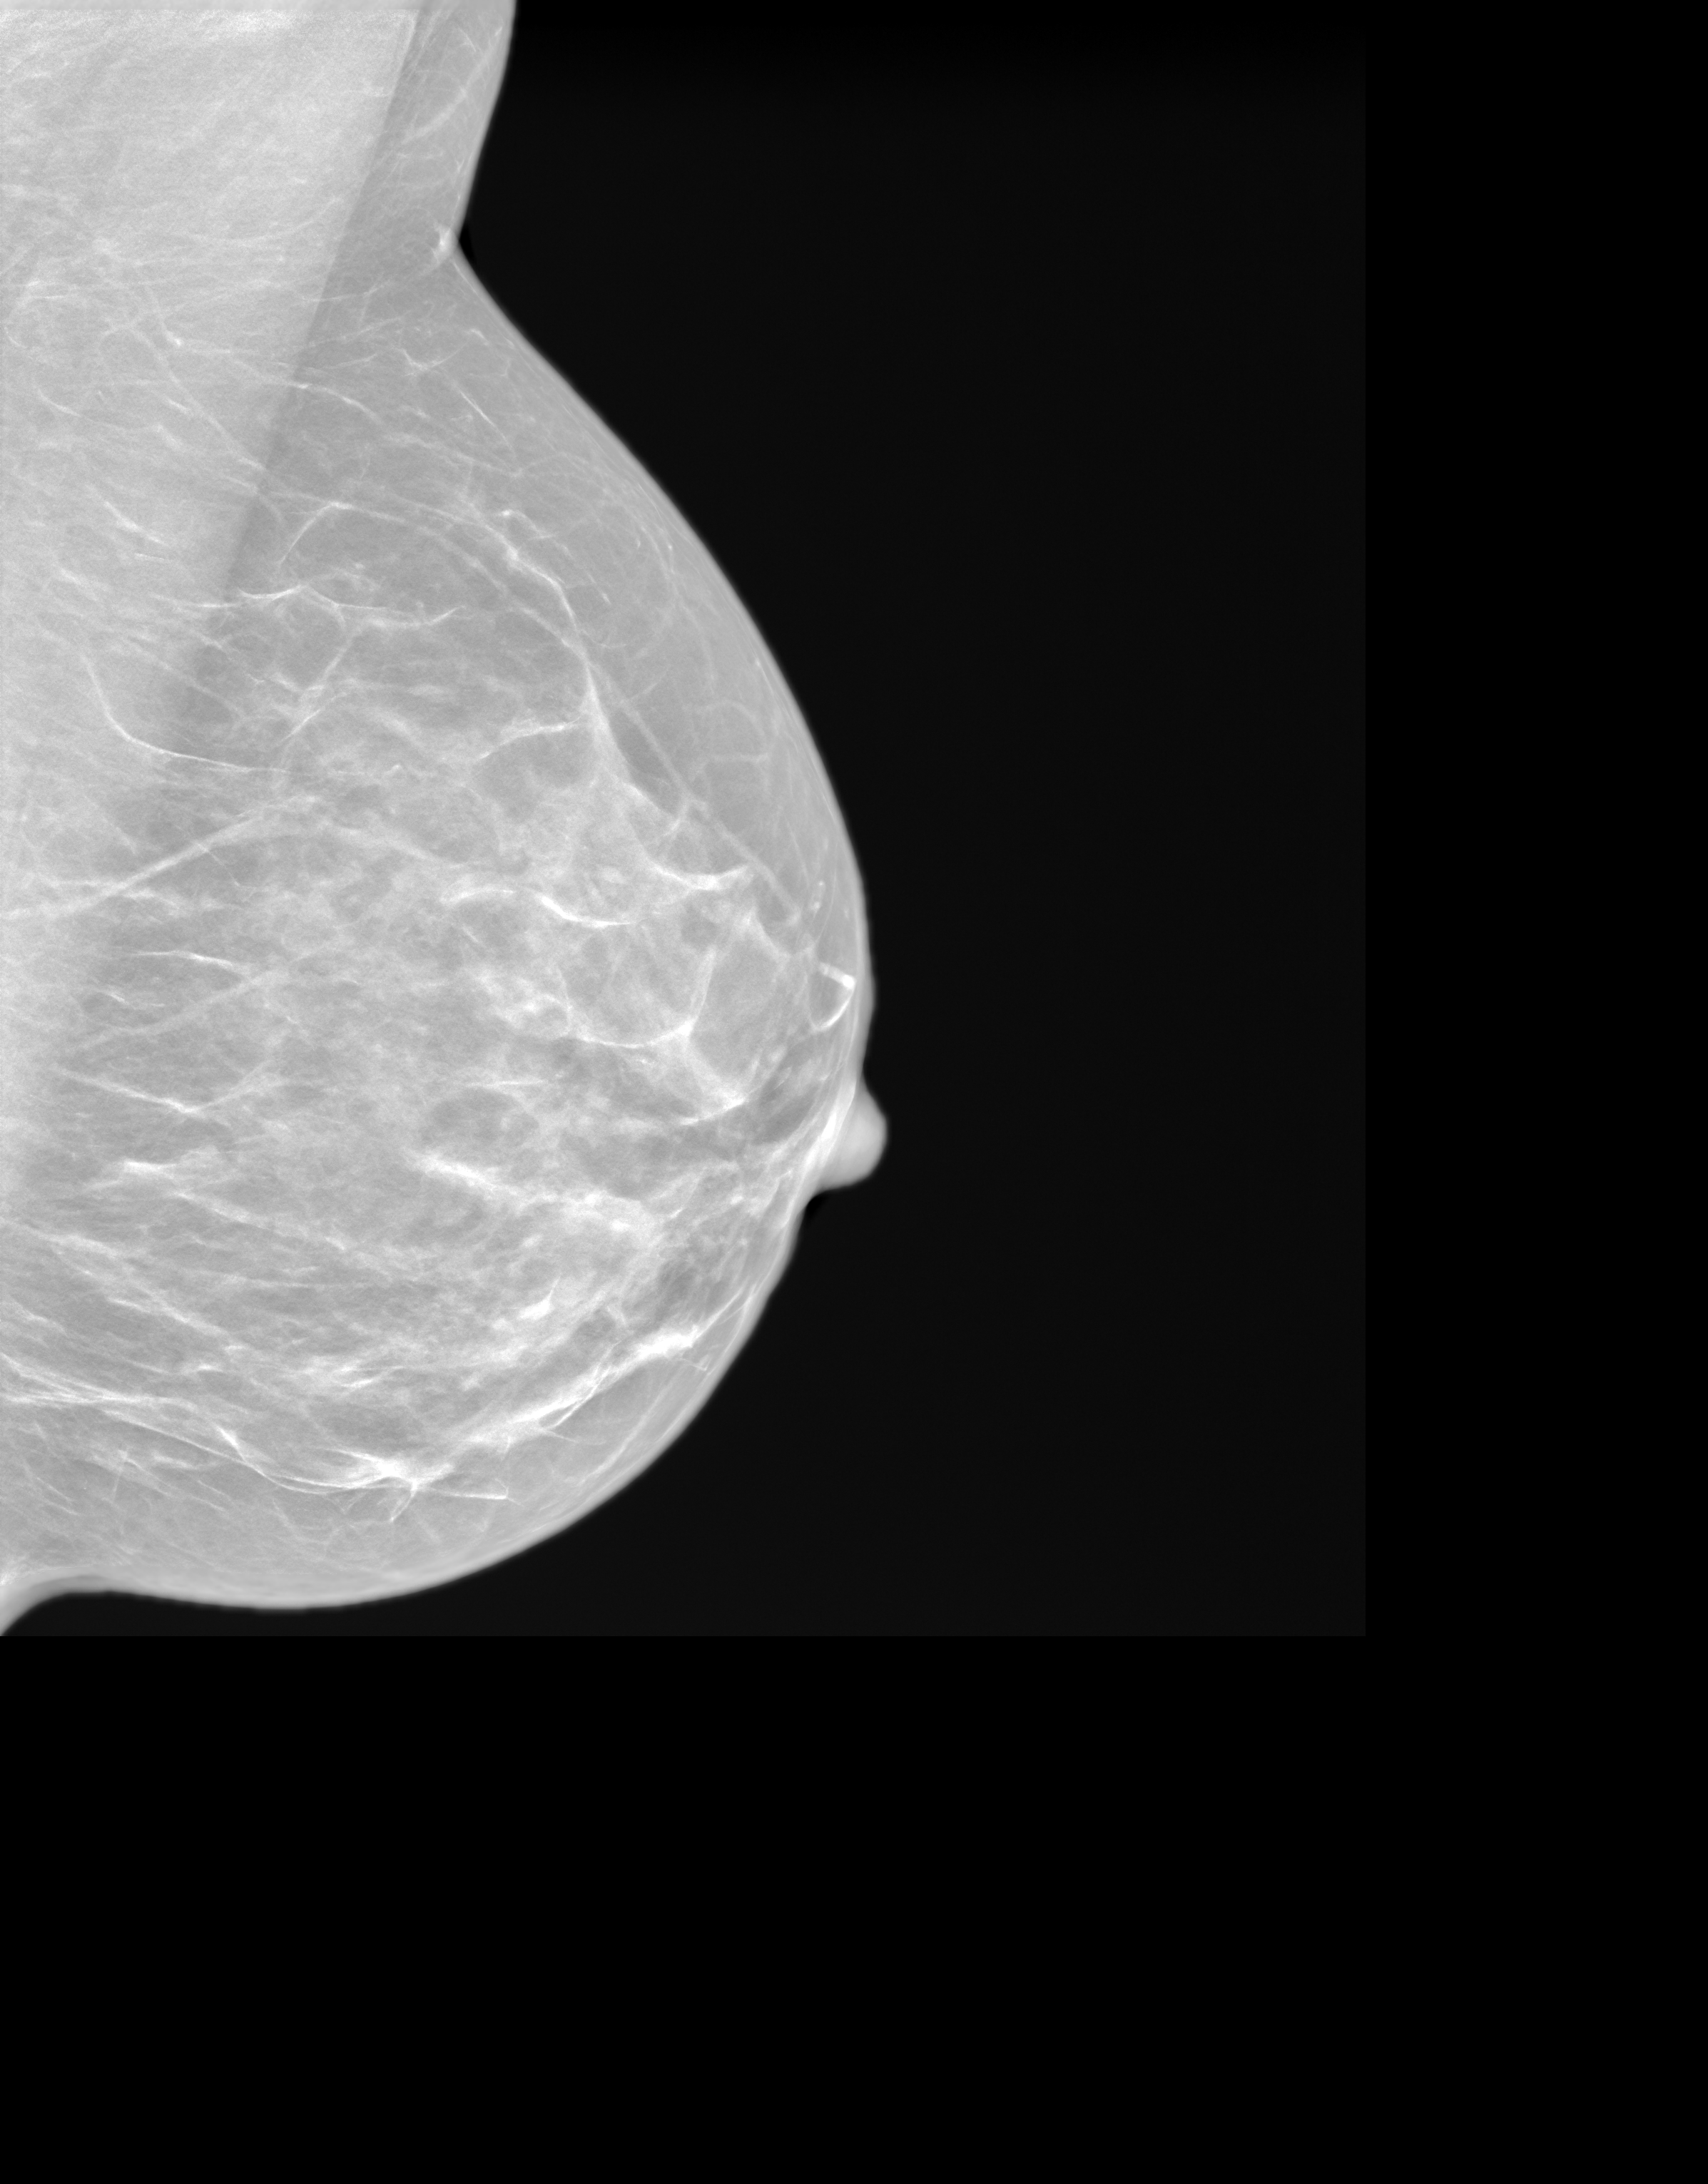
Synthesized 2-D mammogram reconstructed from digital breast tomosynthesis; left breast; medio-lateral oblique projection; screening examination. Patient aged 53 years (female).
BI-RADS breast density category at the screening exam (both breasts, scale 1–4): 3. Final BI-RADS category for the screening round (tomosynthesis exam, both breasts): category 1. Recall: no recall after this screen.